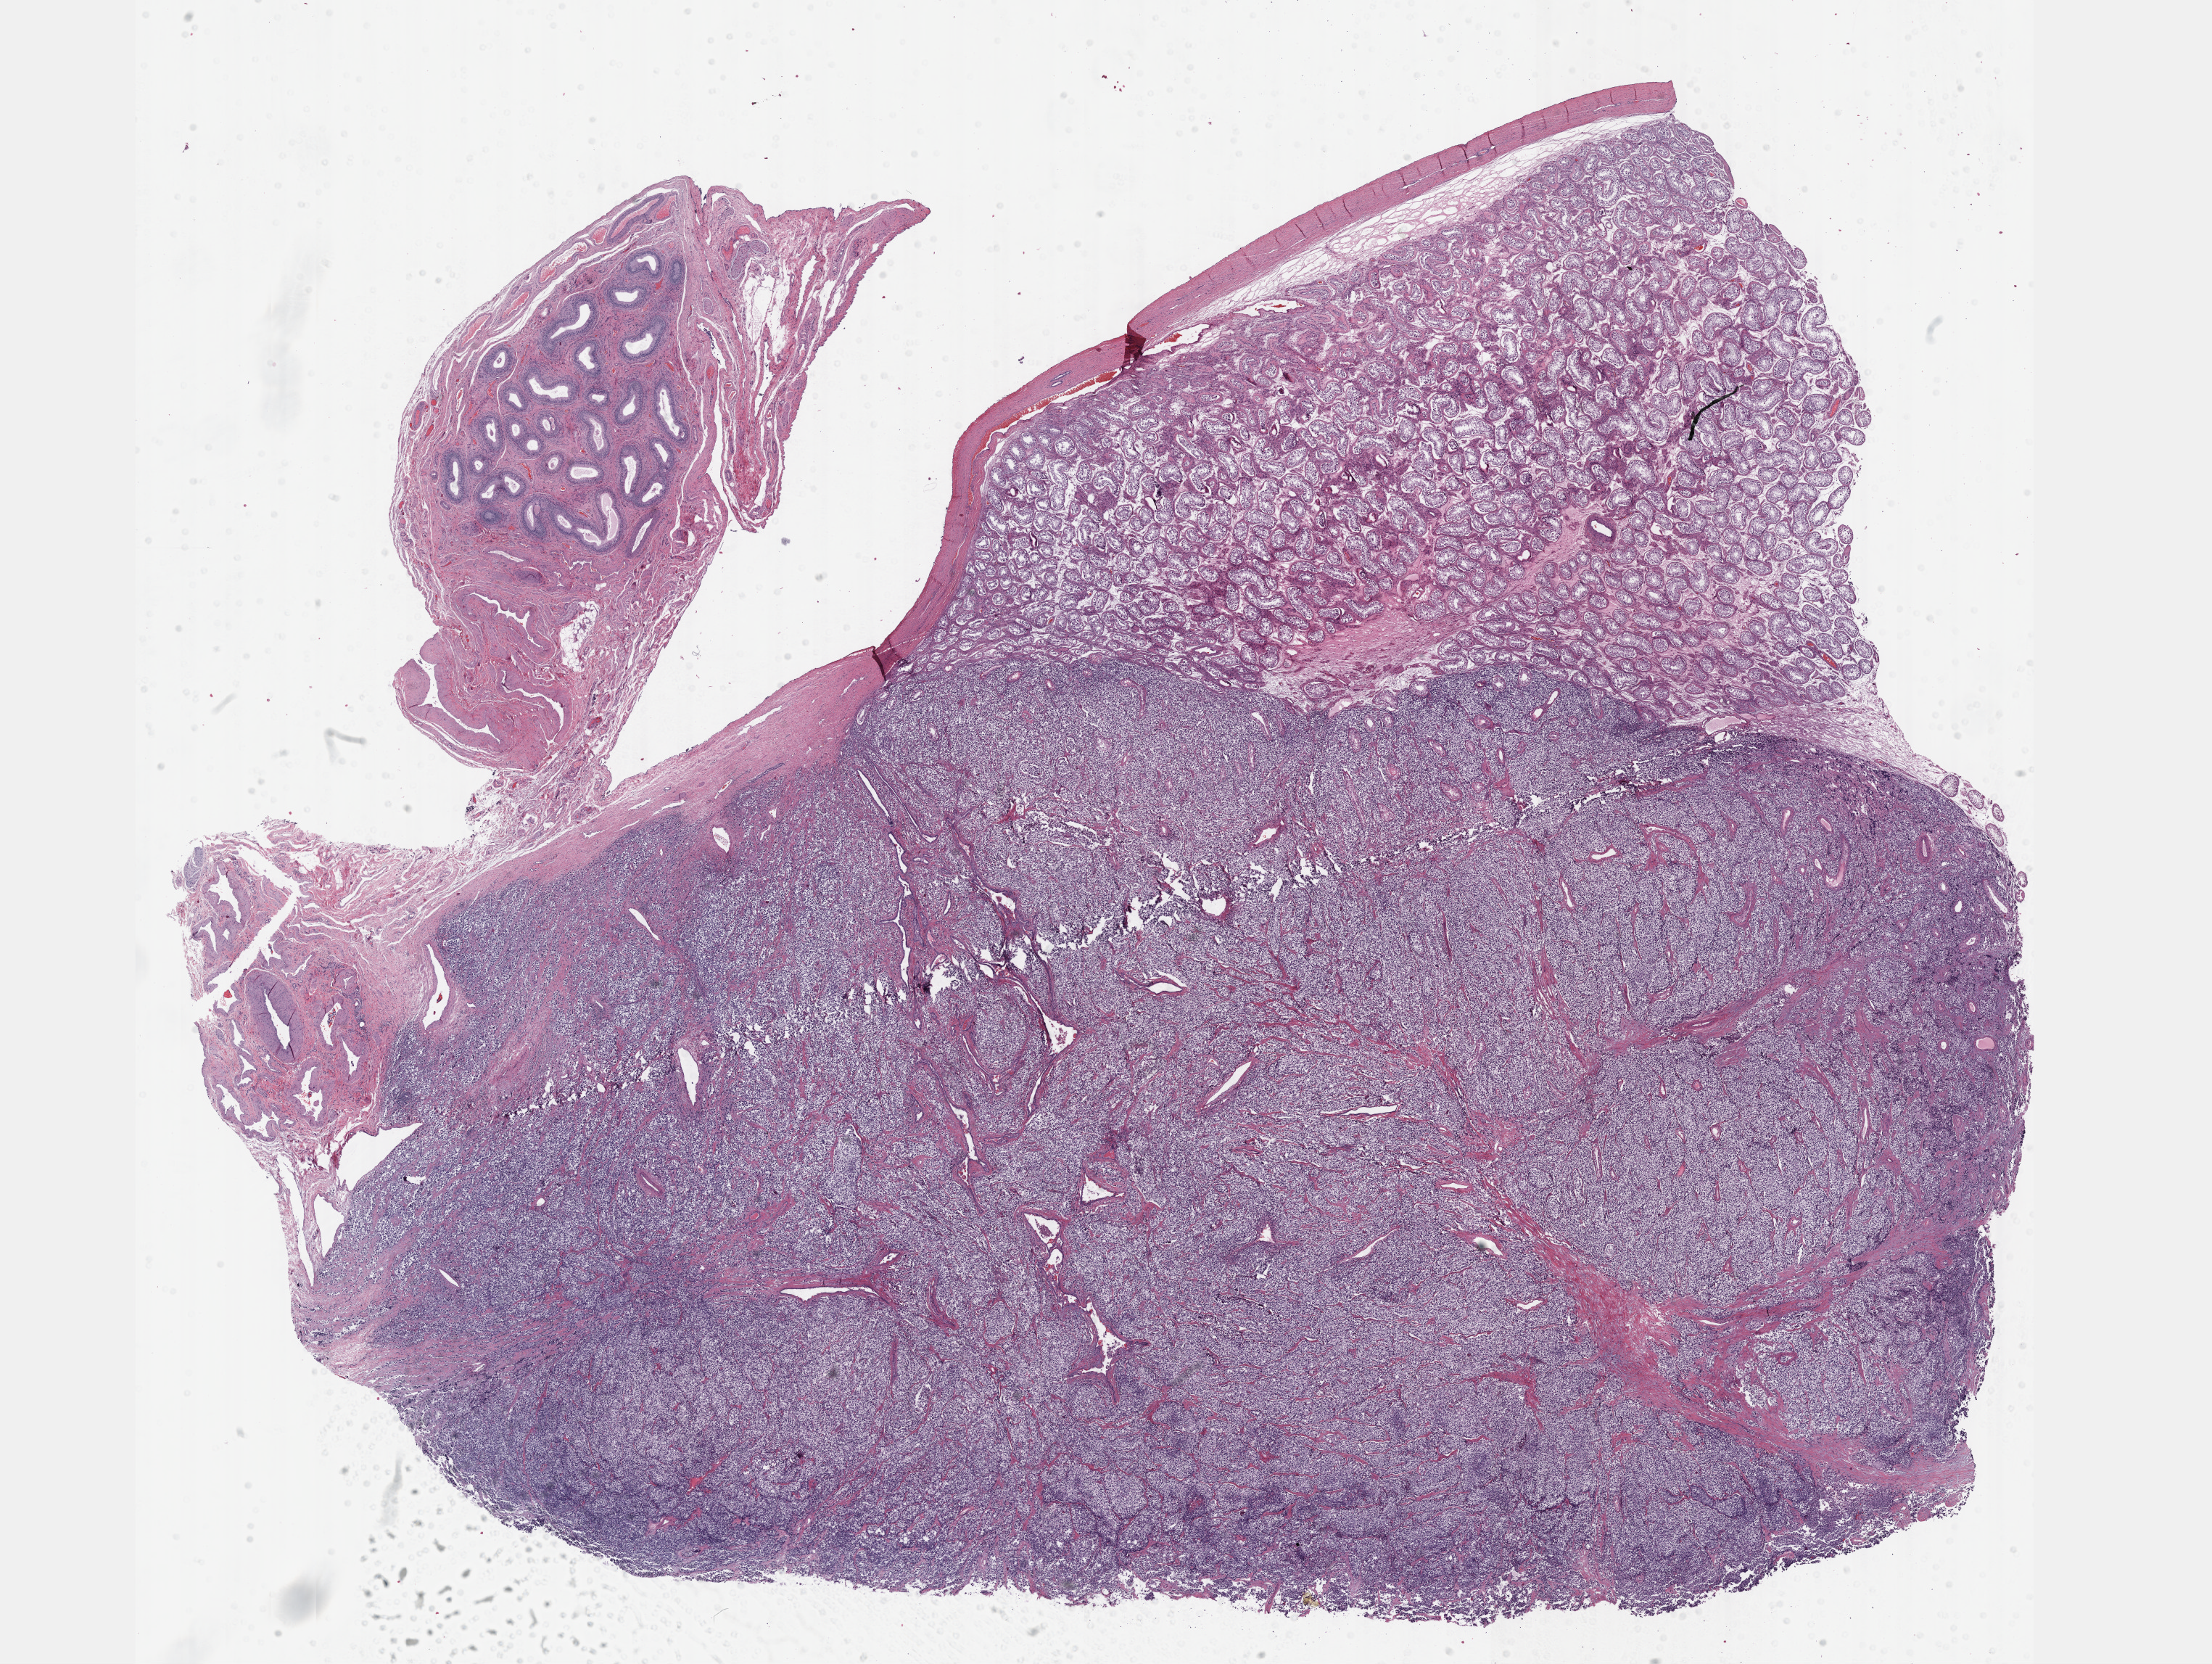
Whole-slide histology image, H&E, whole scanned area (about 24.6 x 18.5 mm) shown as a low-resolution overview; formalin-fixed paraffin-embedded (FFPE) diagnostic section; sample: primary tumour, testis. Male, age 27 years at initial diagnosis.
Laterality: right. Diagnosis: Seminoma, NOS. TNM: T2 NX M0. AJCC pathologic stage: IB (7th edition).